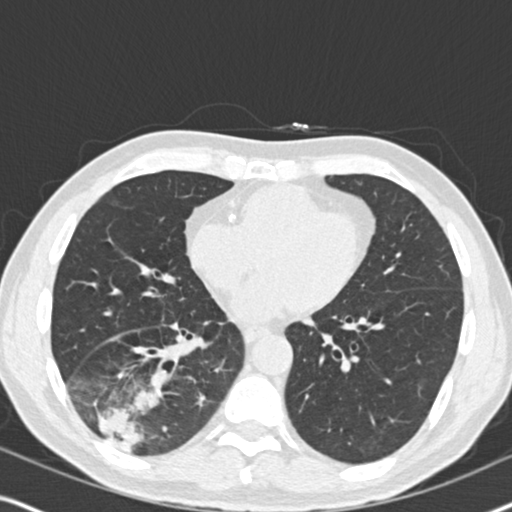
Low-dose screening chest CT, one axial slice; position 81 of 182 along the scan axis; reconstruction kernel B30f; 120 kVp; lung window (W 1500 / L -600 HU); 2 mm slice thickness; 512 × 512 image matrix, field of view 330 × 330 mm.
Structures marked on this image (expert manual segmentation):
- lesion 1 (tumor, lower lobe of right lung): box from (x=99, y=389) to (x=158, y=450) px